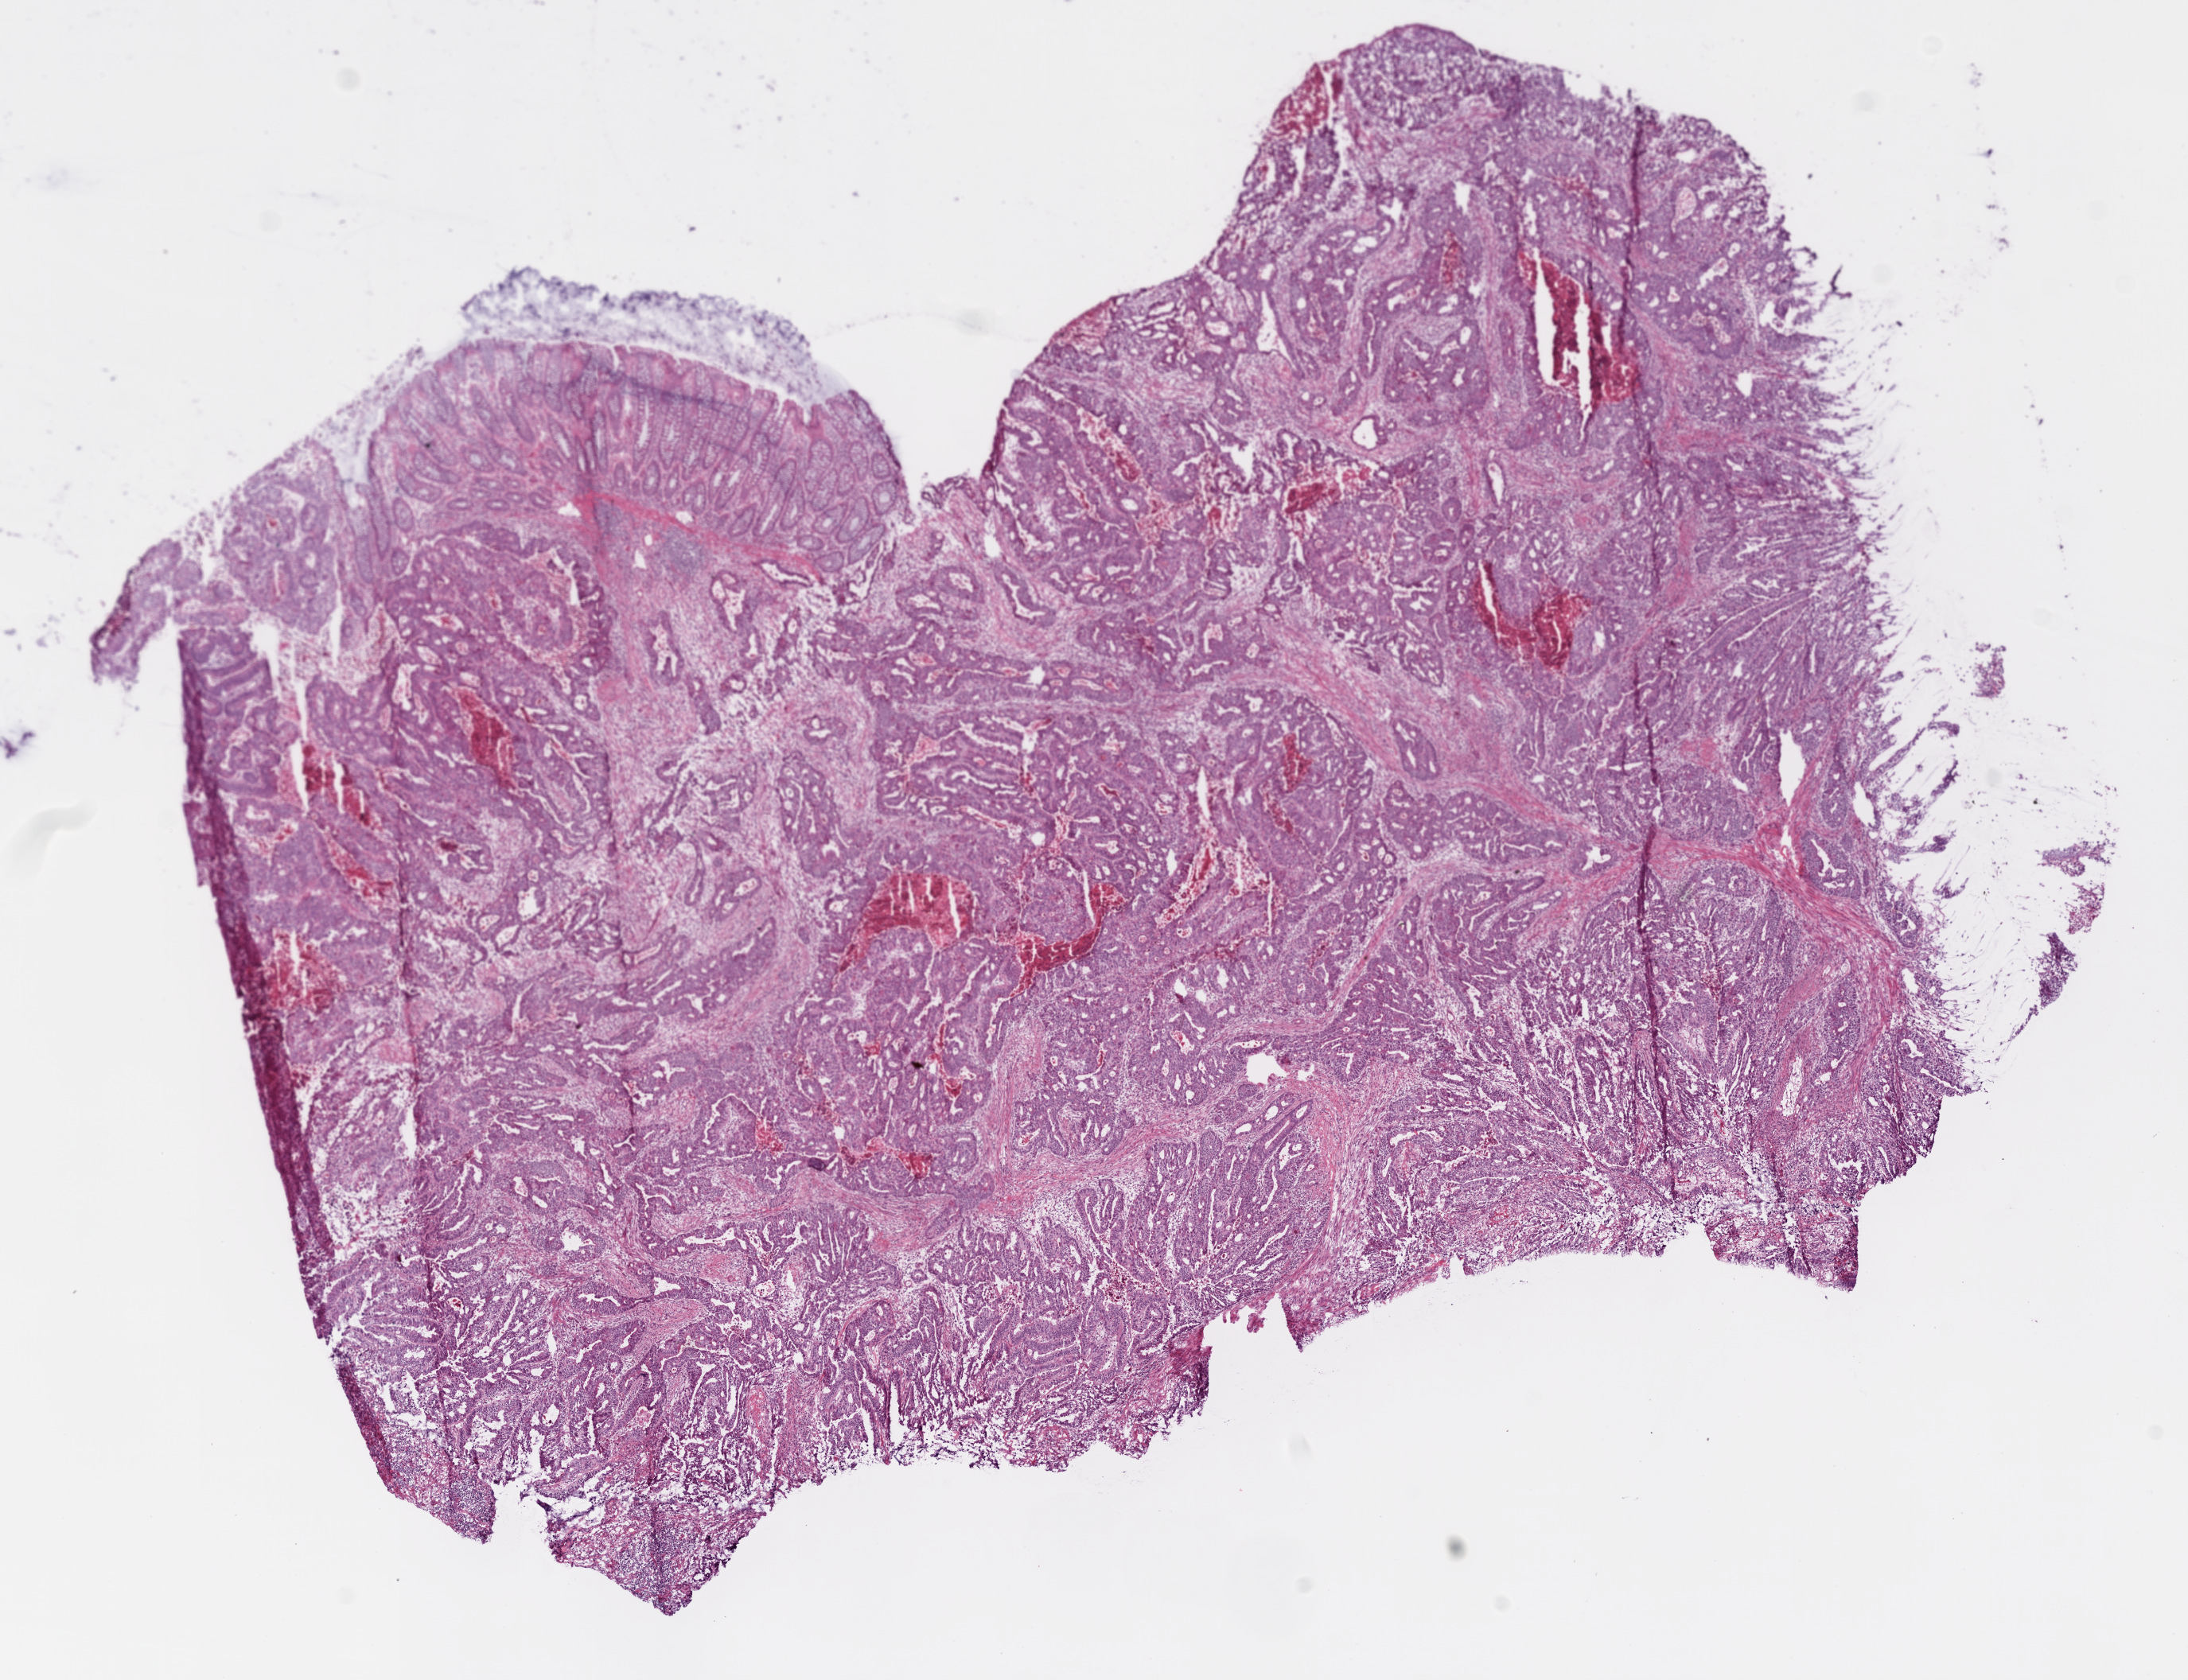
Whole-slide histology image, Hematoxylin and eosin (H&E) stained — shown as a low-resolution overview of the whole scanned area (about 11.0 x 8.5 mm); frozen section from the bottom of the tissue portion; primary tumour sample from the colon. Male patient; age at initial diagnosis 66 years. Composition of this section per pathologist review: tumour cells 83%, tumour nuclei 80%, normal cells 5%, stromal cells 10%, necrosis 12%.
AJCC pathologic stage: IIA (6th edition). Diagnosis: Adenocarcinoma, NOS. Lymph nodes positive (case pathology): 0 of 24 examined.